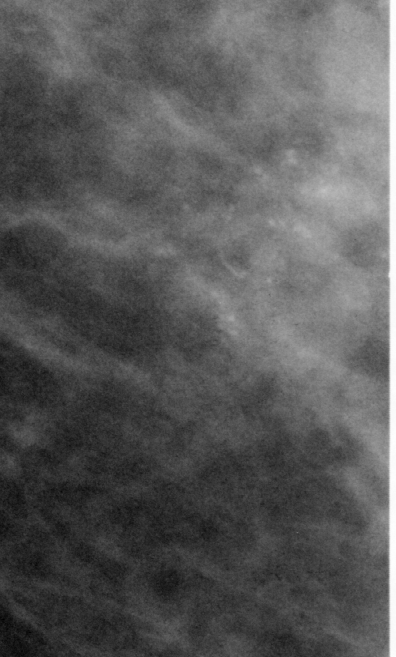
Crop from a digitized film mammogram around one marked abnormality, right breast, CC view, BI-RADS breast density category 2 (scale 1–4).
- Marked abnormality: calcifications, morphology pleomorphic, distribution clustered; BI-RADS assessment category 5; subtlety rating 4 on a 1 (subtle) to 5 (obvious) scale; pathology (as recorded): malignant.